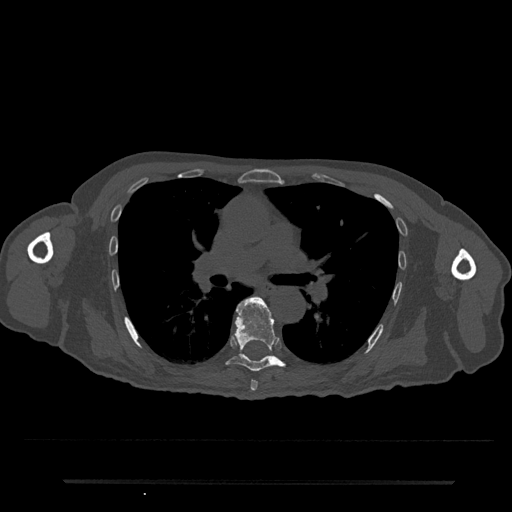
CT including the spine, one axial slice; reconstruction kernel Br40s/3; 120 kVp; bone window (W 1800 / L 400 HU); 512 × 512 image matrix, field of view 427 × 427 mm. Male patient, age 74 years. Case-level facts recorded for this patient, not image findings: primary cancer: prostate.
Annotated regions visible in this slice (semi-automatically segmented with operator editing):
- T6 vertebra: bounding box (x1, y1, x2, y2) in pixels: (250, 380, 258, 391)
- T7 vertebra: (225, 297, 284, 372)